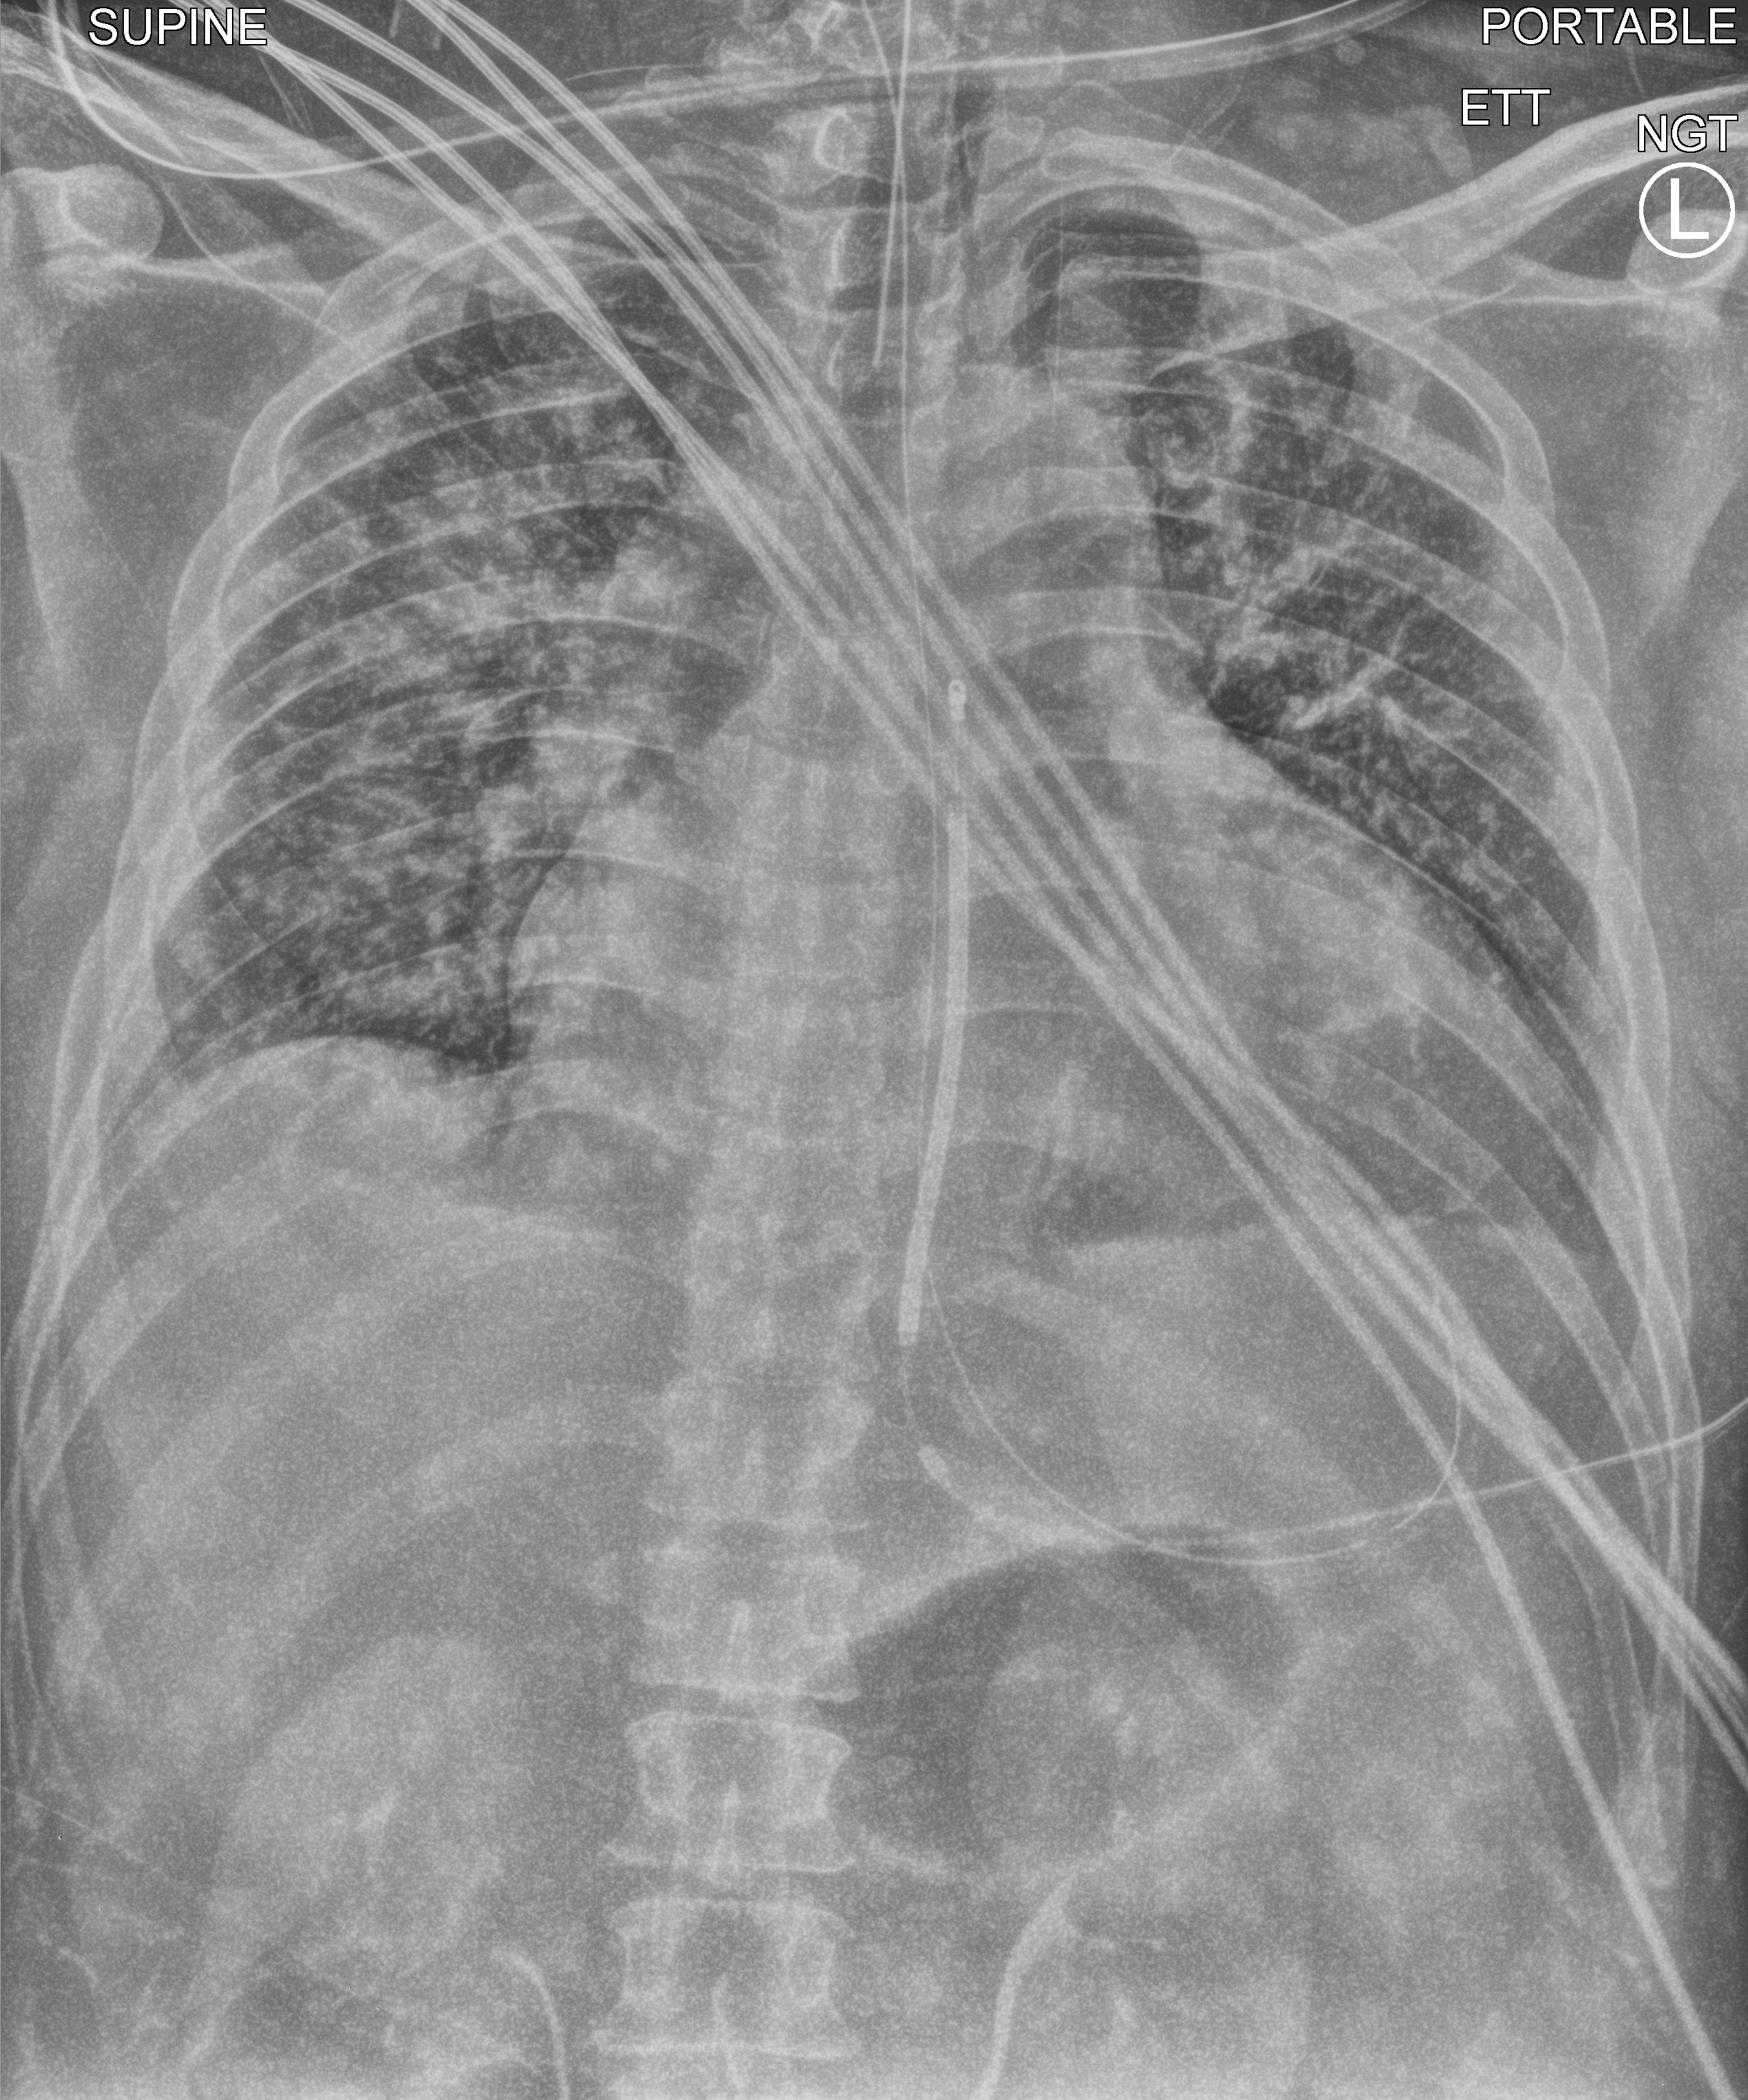
Portable chest radiograph; anteroposterior (AP) projection. Male patient hospitalised with COVID-19, age 18–59 years.
Hospital-stay facts (about this admission, not read from this image; timing relative to this image not recorded): mechanically ventilated during this hospital stay: no; length of hospital stay: 19 days.